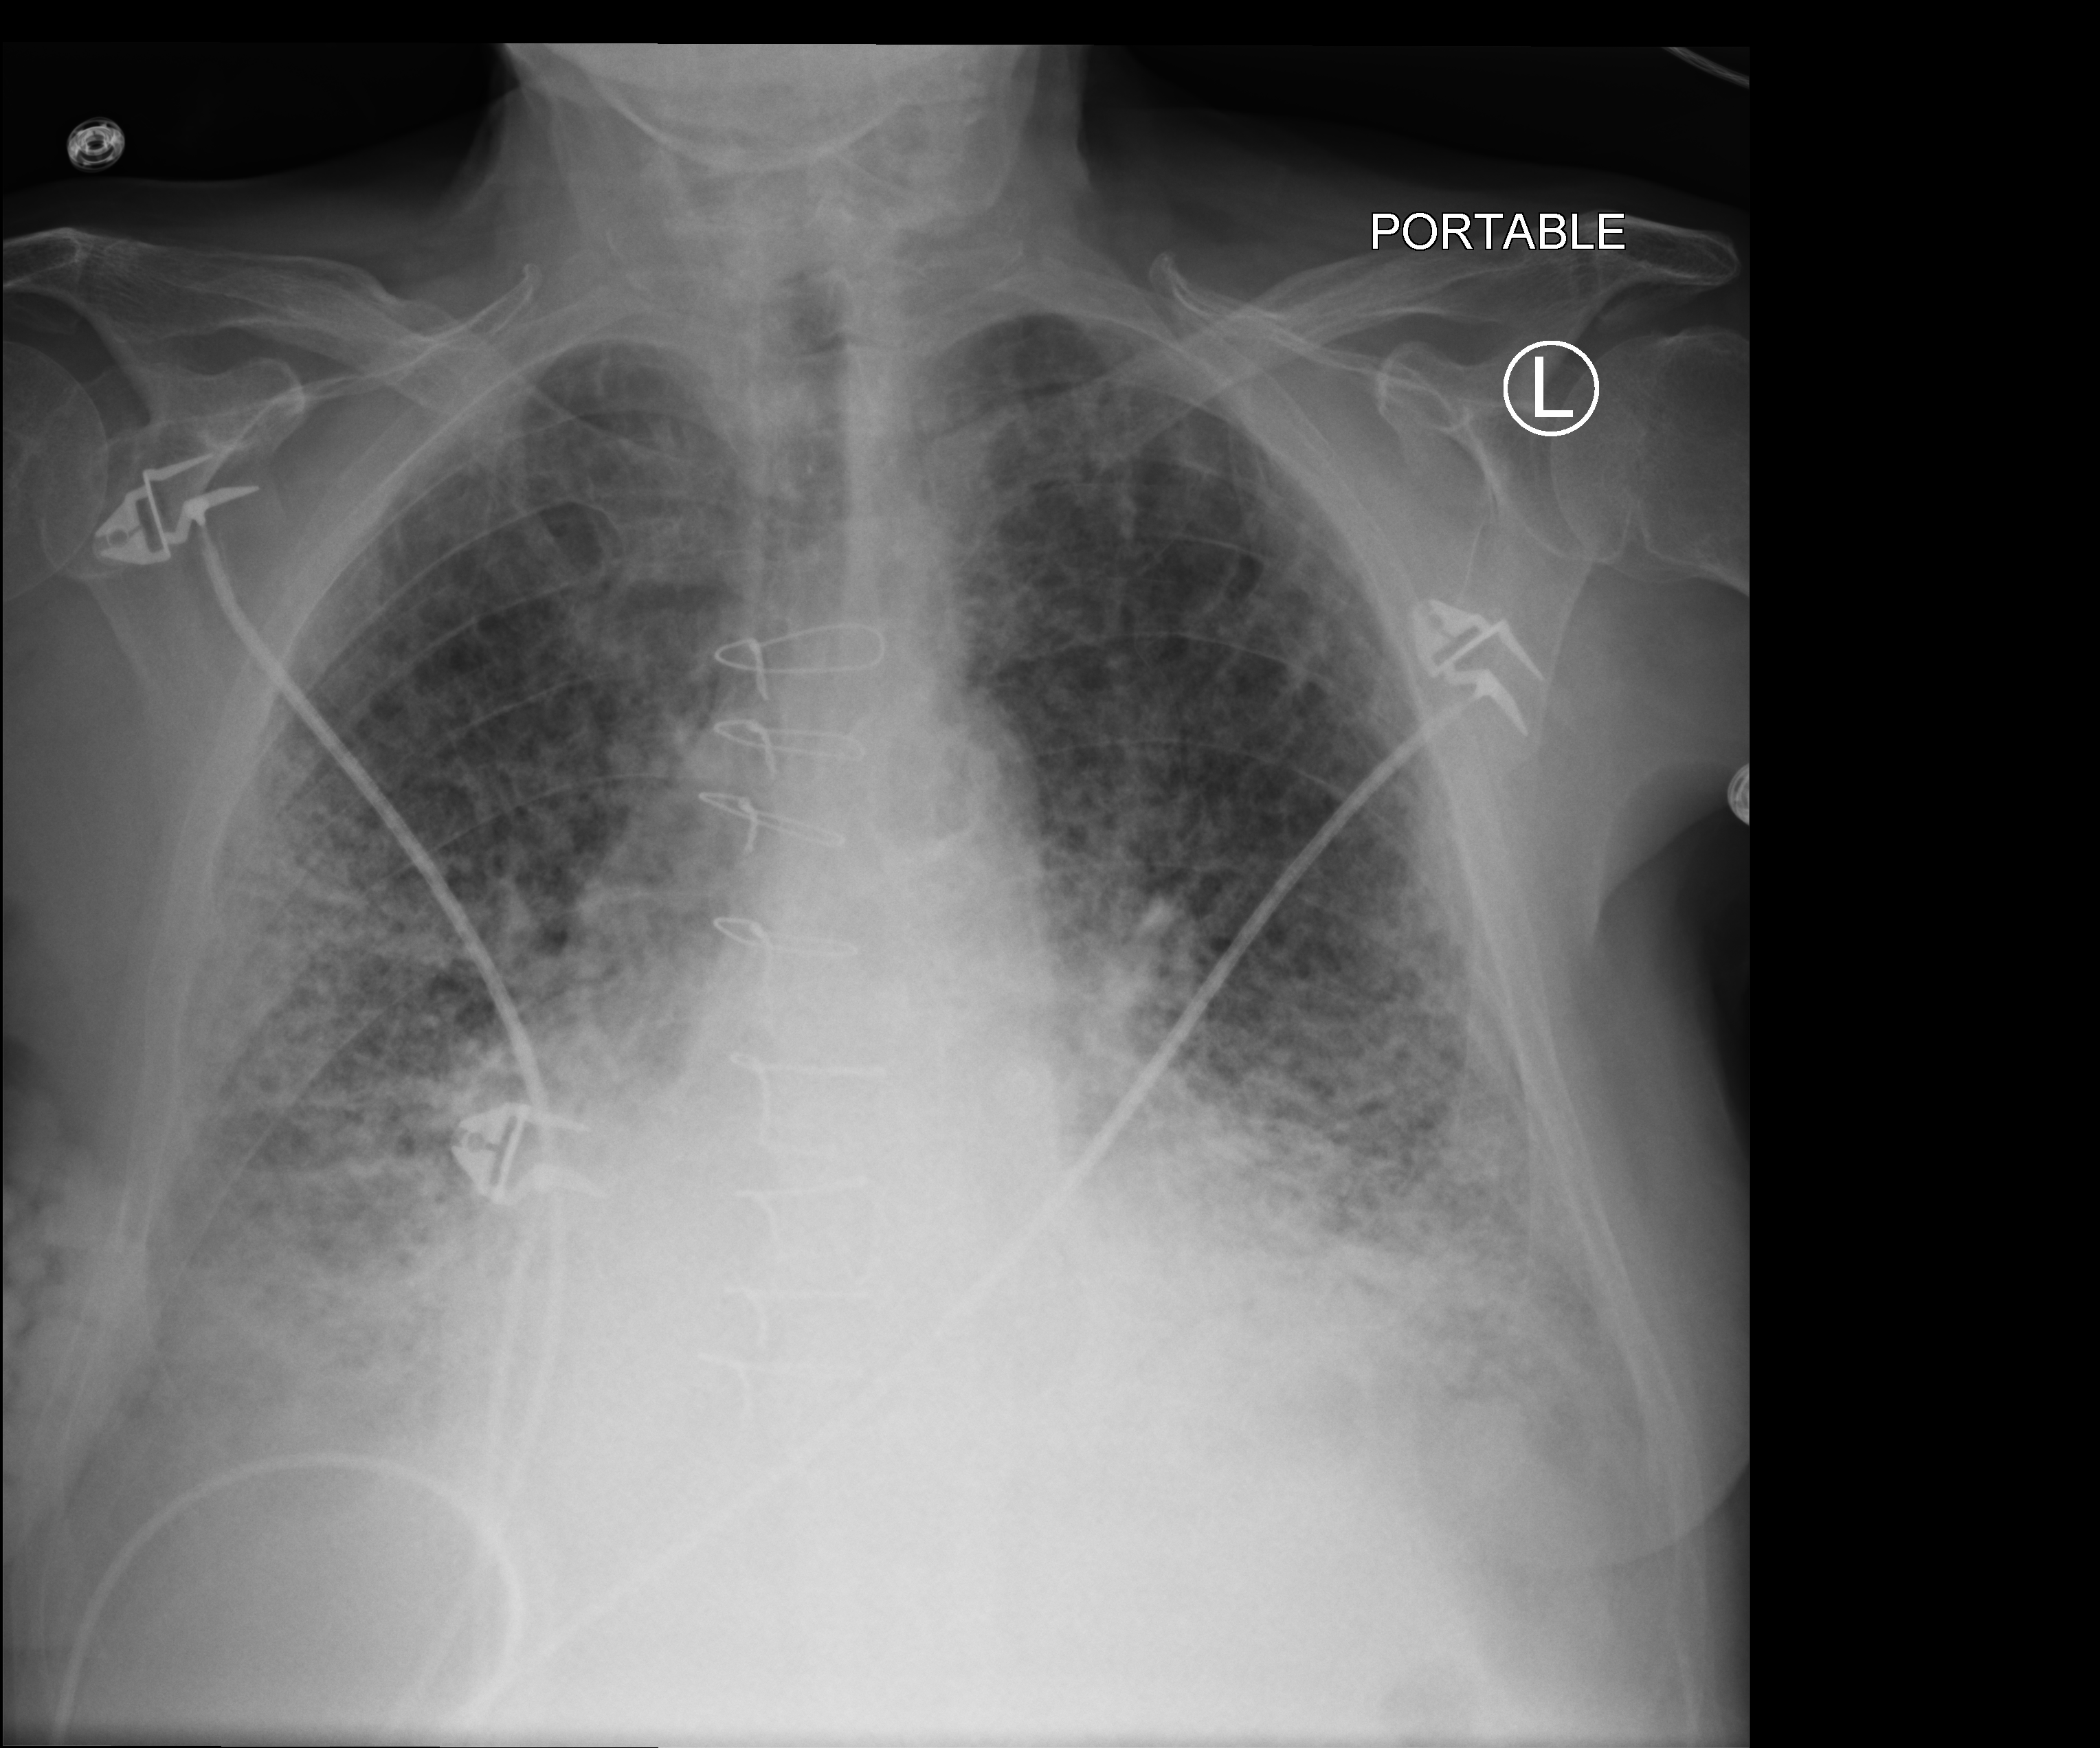
Bedside chest radiograph (computed radiography), anteroposterior (AP) projection. Patient hospitalised with COVID-19; male, aged 75–90 years.
Hospital-stay facts (about this admission, not read from this image; timing relative to this image not recorded): mechanically ventilated during this hospital stay: yes; admitted to intensive care during this hospital stay: yes.